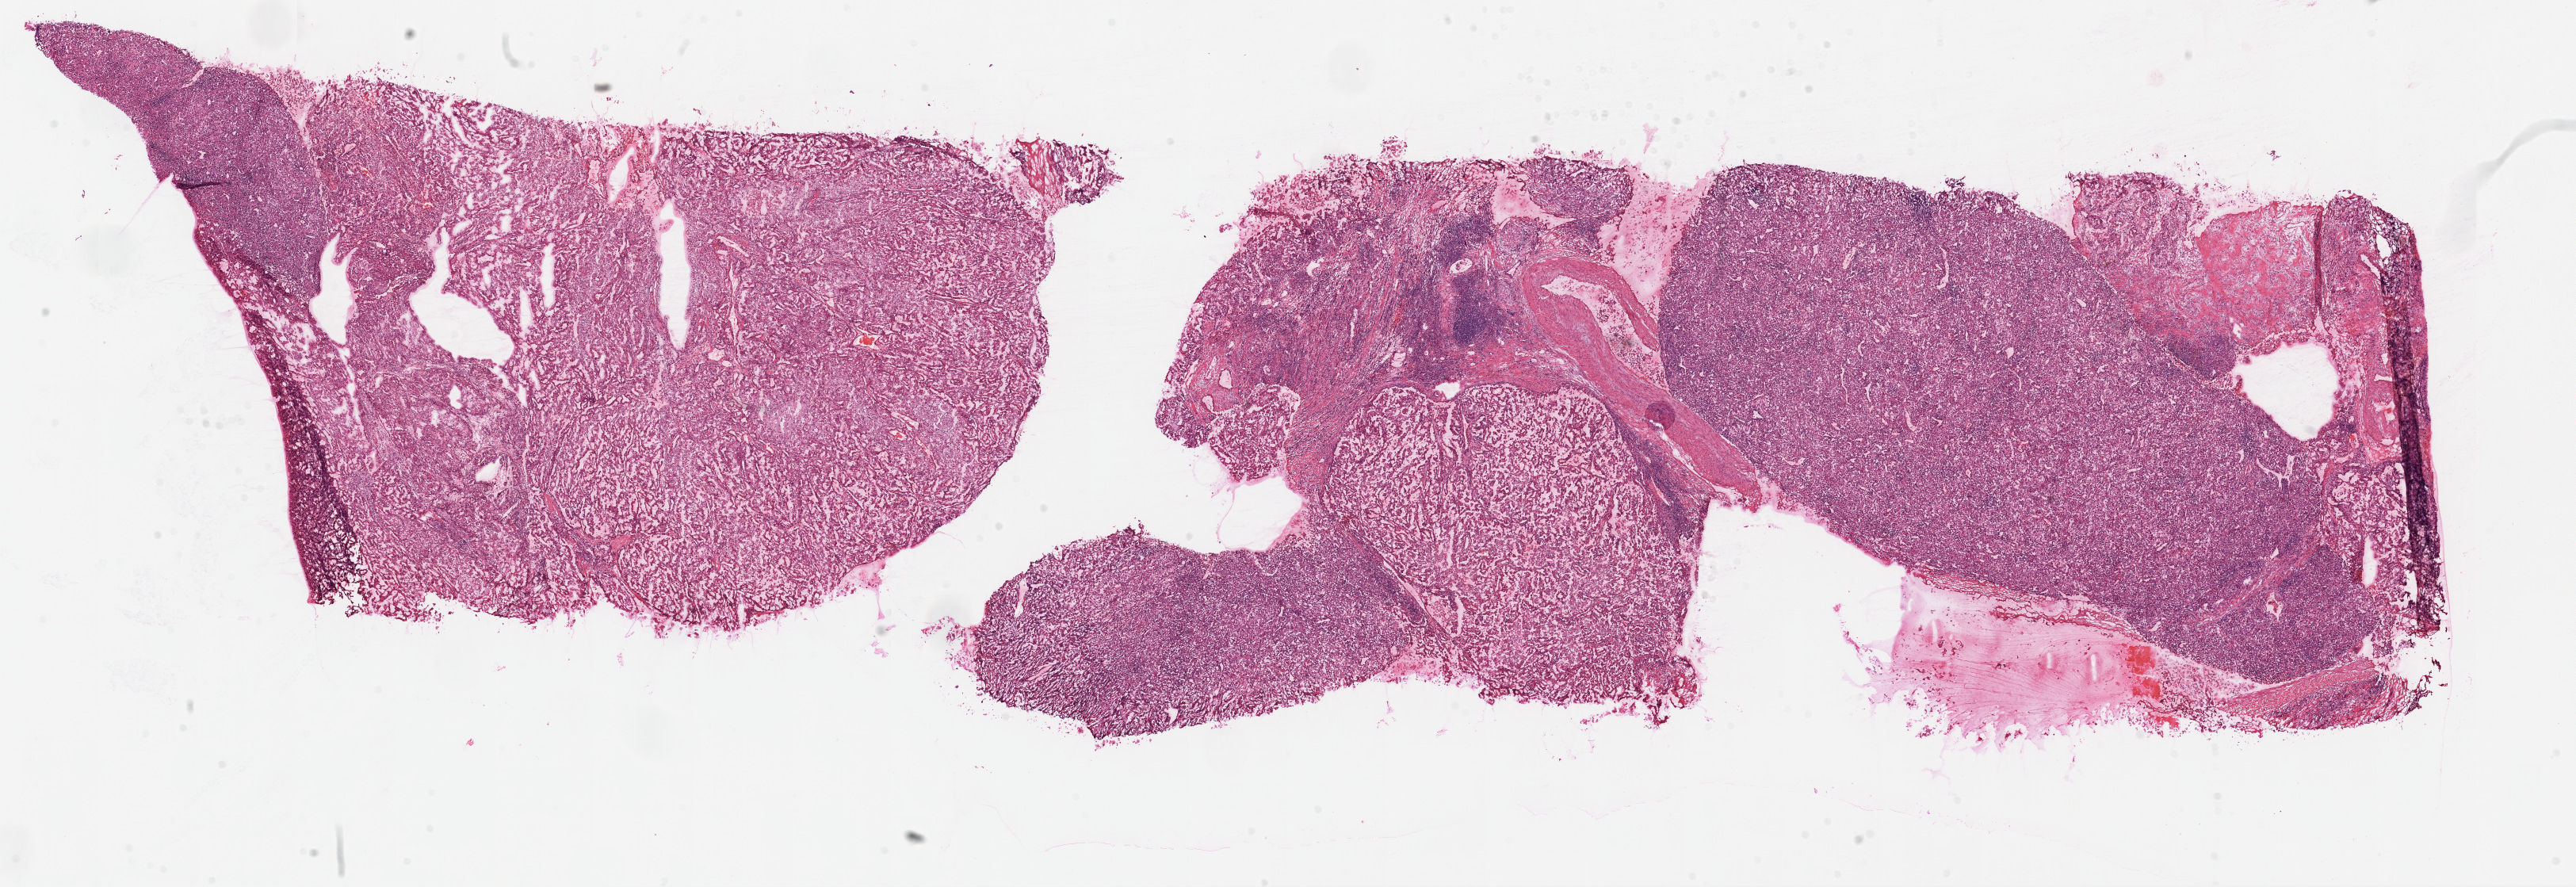
Digitized H&E-stained tissue section (whole slide), whole scanned area (about 26.1 x 9.0 mm) shown as a low-resolution overview; frozen section from the top of the tissue portion; primary tumour sample from the kidney. Patient: female, age at initial diagnosis 55 years. Histologic grade: G4 (undifferentiated). Composition of this section per pathologist review: tumour cells 85%, tumour nuclei 75%, normal cells 0%, stromal cells 15%, necrosis 0%.
* pathologic diagnosis: Clear cell adenocarcinoma, NOS
* AJCC pathologic stage: IV
* TNM: T3a NX M1
* laterality: left